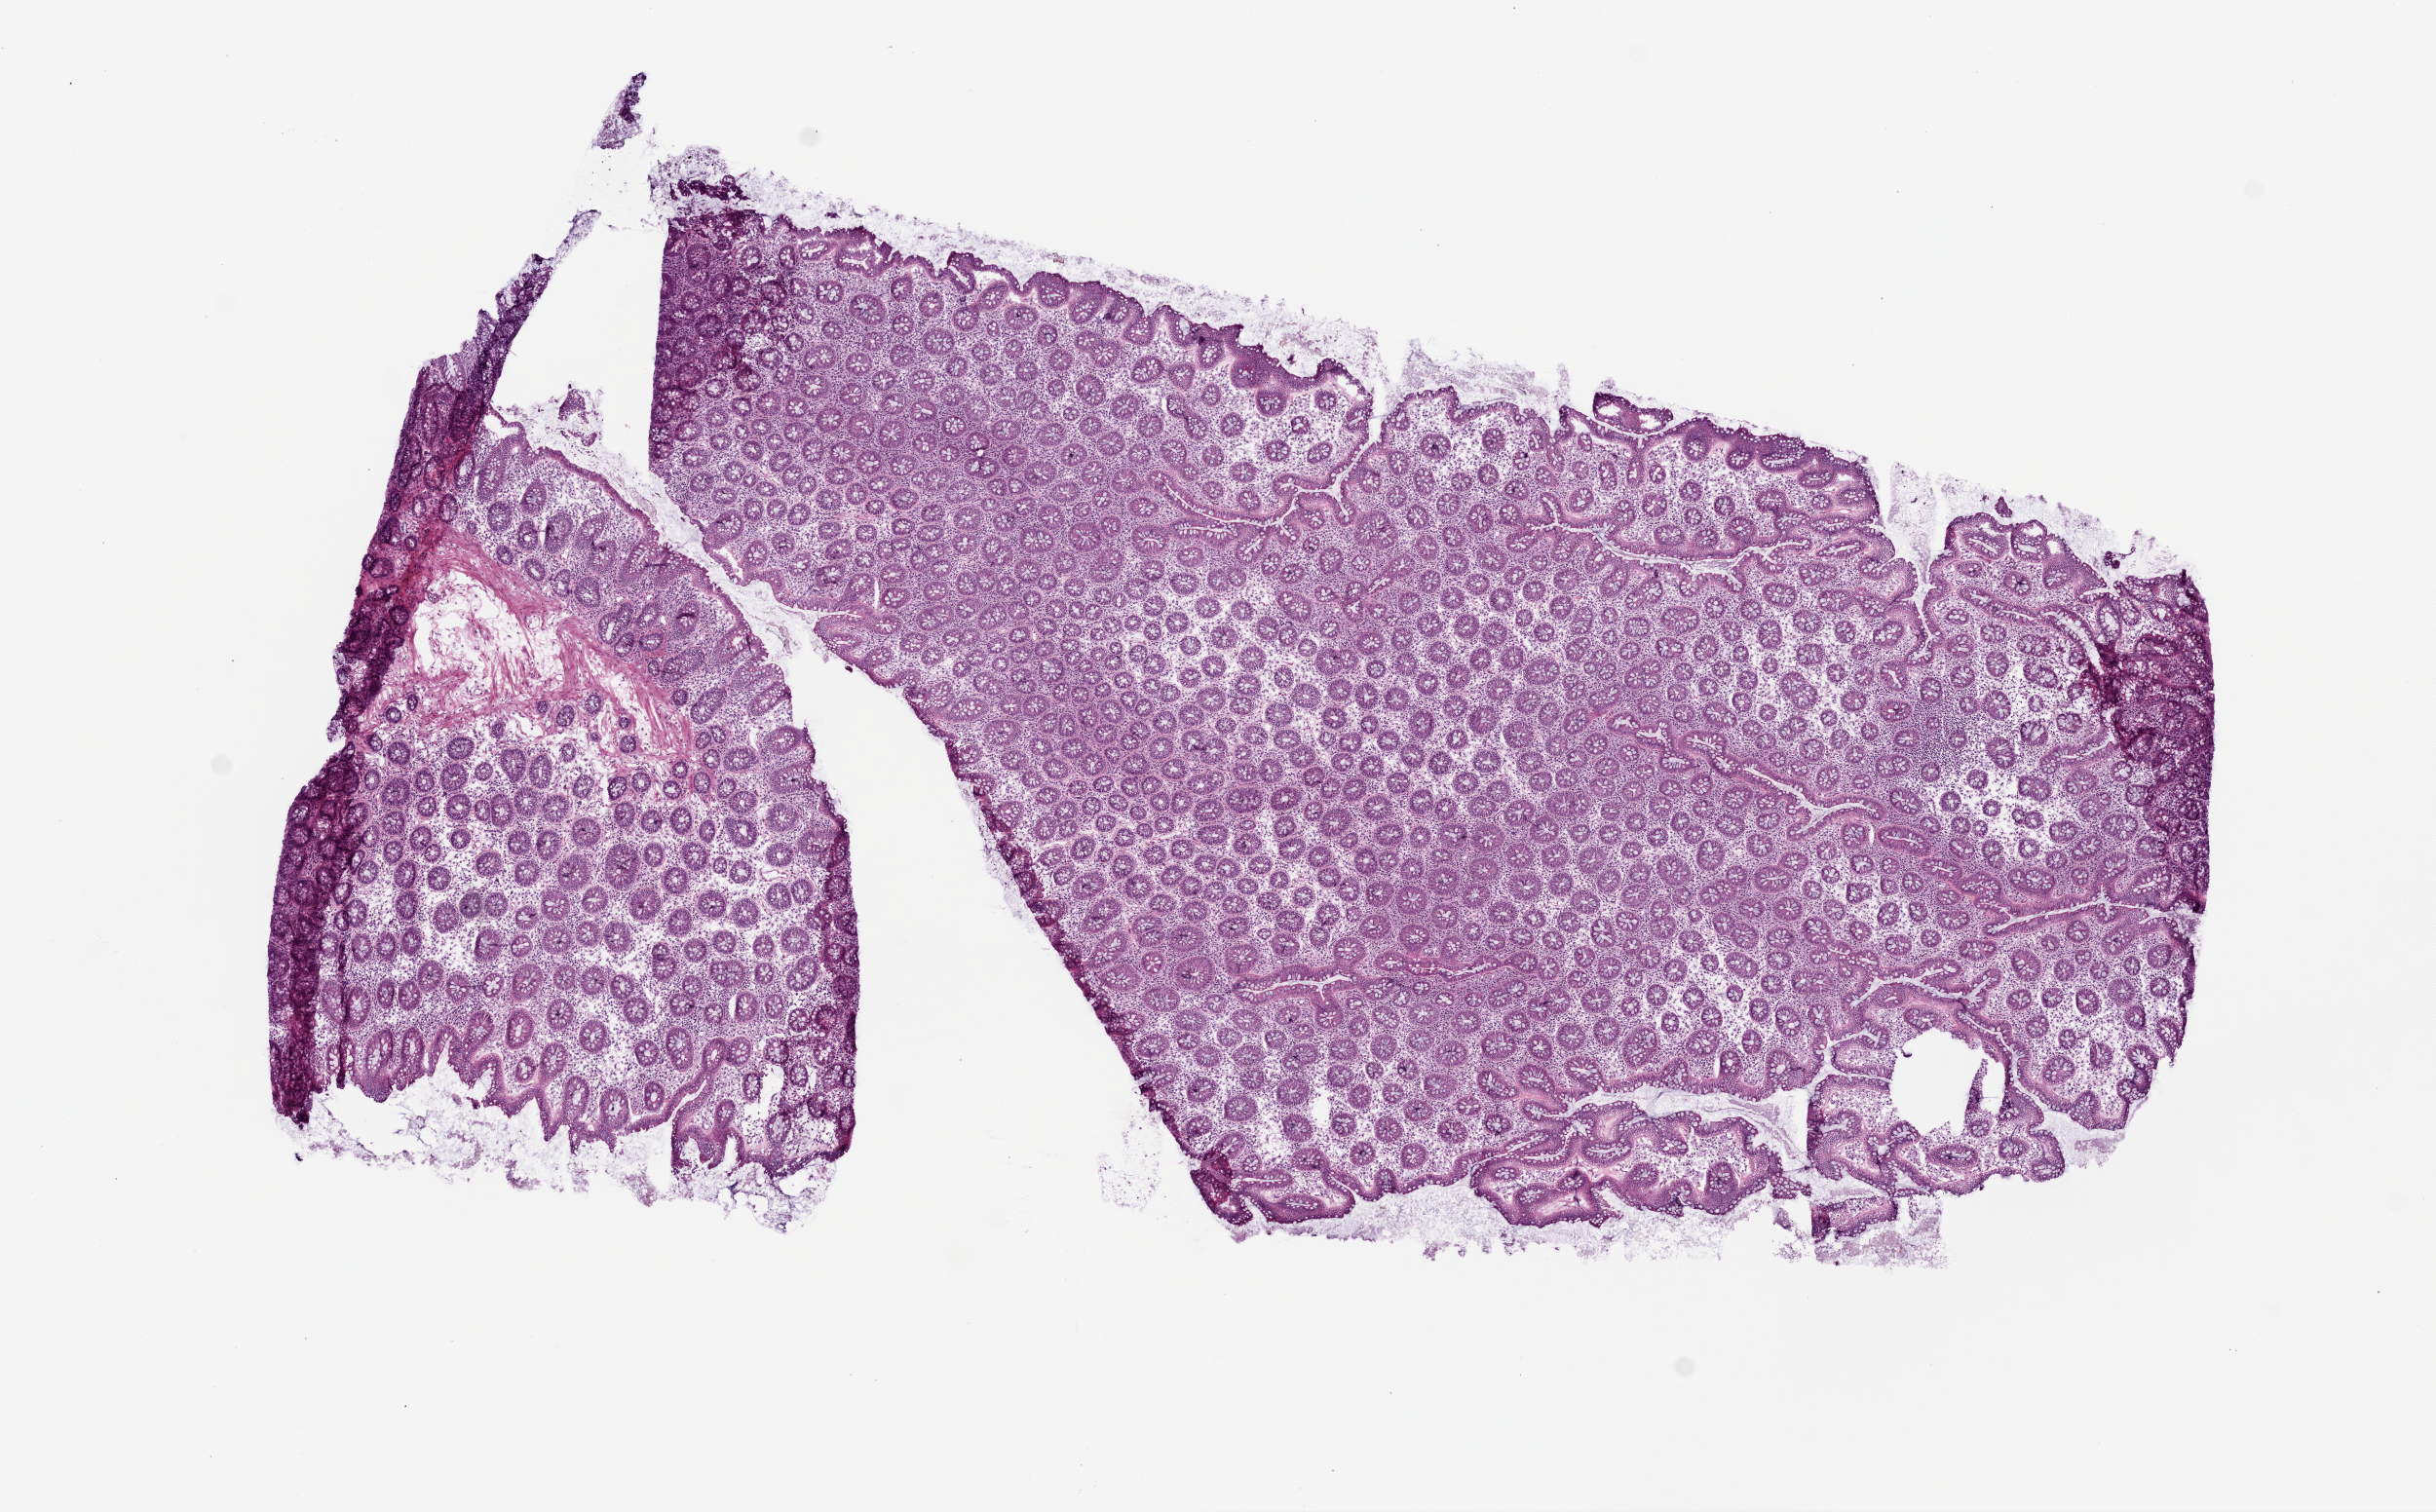
Digitized Hematoxylin and eosin (H&E) stained tissue section (whole slide), a low-resolution overview of the entire scanned area, about 10.0 x 6.2 mm (acquisition: 20x scan). Frozen section from the top of the tissue portion. Colon, solid tissue normal (non-tumour tissue) sample. Female, age 80 years at initial diagnosis.
This section: solid tissue normal sample (biorepository sample class). Patient diagnosis: Adenocarcinoma, NOS (ascending colon).